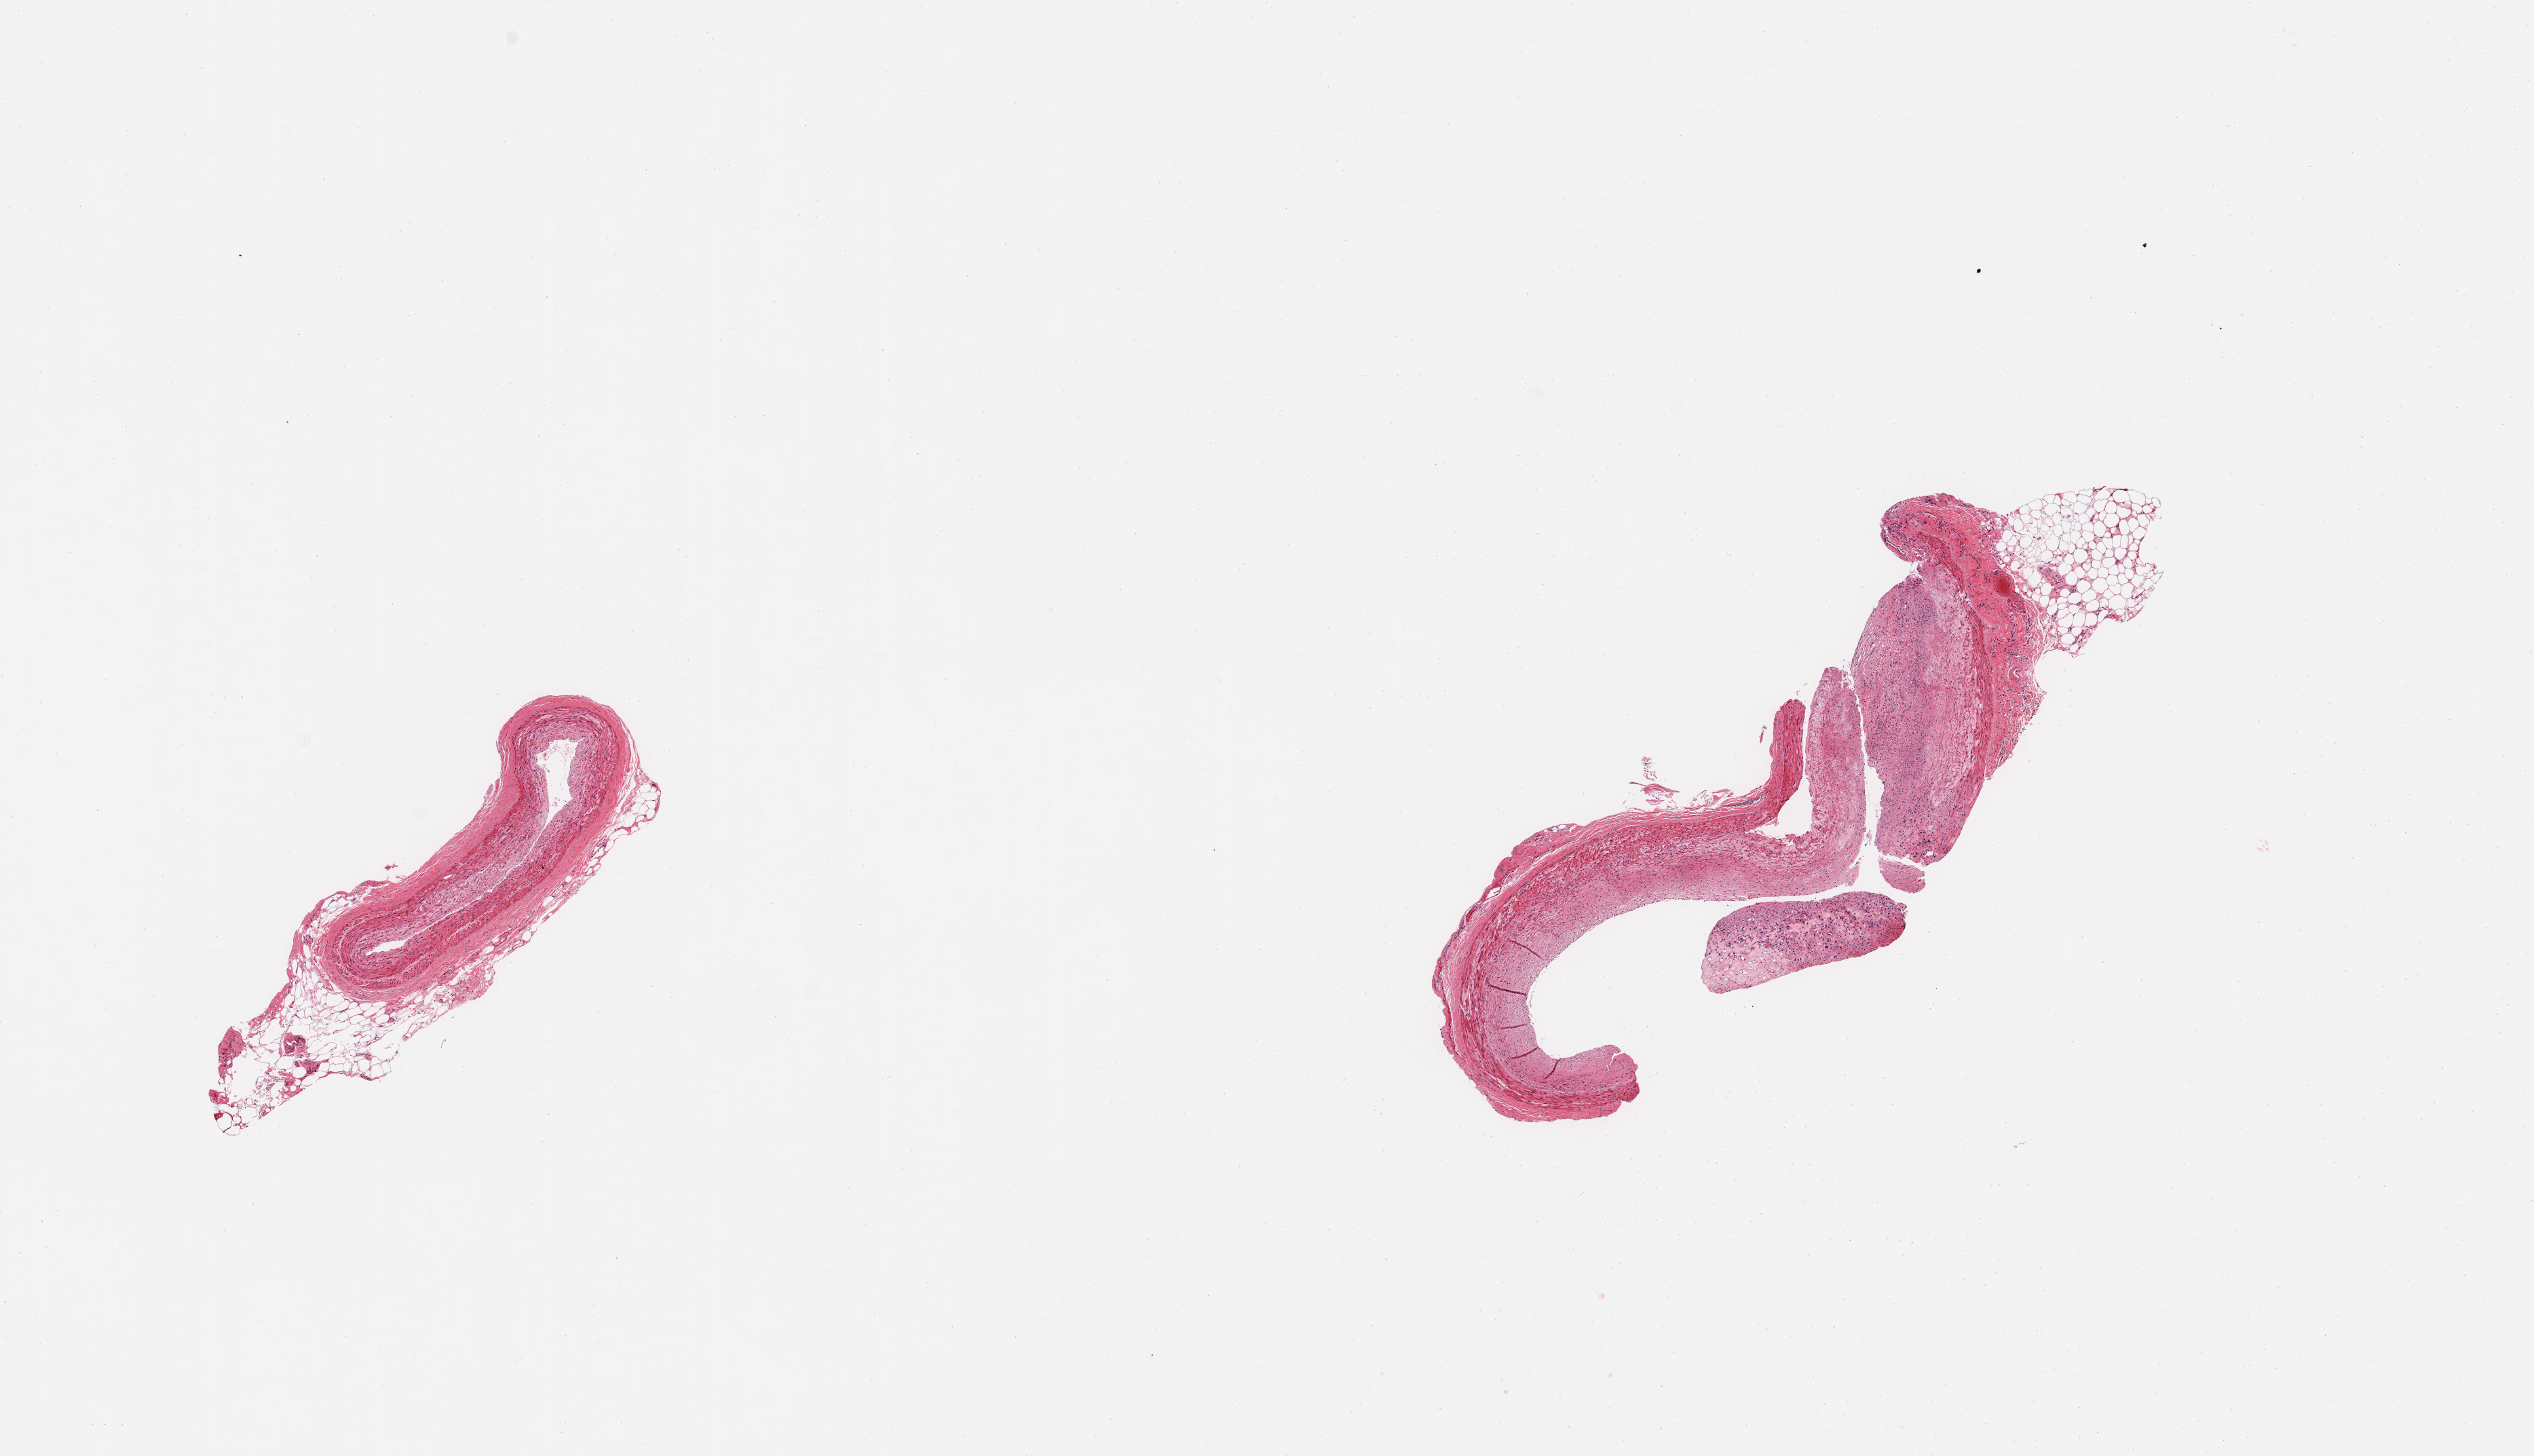
Haematoxylin and eosin whole-slide image, whole scanned area (about 14.8 x 8.5 mm) shown as a low-resolution overview. PAXgene-fixed paraffin-embedded (PFPE) section. Target tissue: coronary artery. Tissue donor sample. Donor: male.
* reviewer comment on this tissue sample: 2 pieces, nubbins of adherent fat up to ~1mm; minimal atherosis